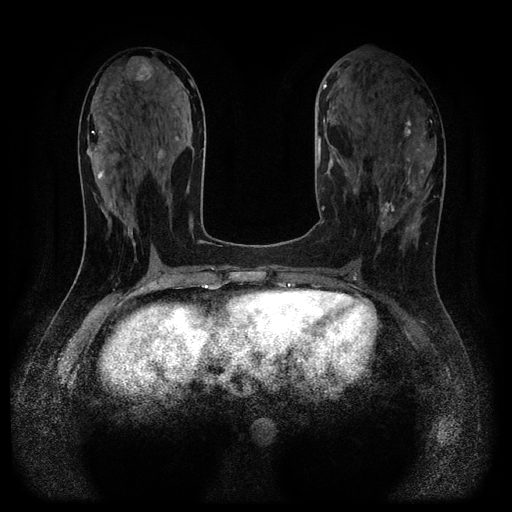
Breast MRI (dynamic contrast-enhanced, multi-phase), one axial slice. Slice 48 of 116 in the series (ordered by position). Dynamic contrast-enhanced series, time point 2 of 5 at this slice position (early post-contrast). 1.5 T. TE 2.7 ms, TR 5.4 ms. 2.2 mm slice thickness. 512 × 512 image matrix. Patient: female, 43 years.
Outlined on this slice (semi-automatic segmentation, software-assisted and operator-edited):
- breast lesion (labelled 'tumour' in the annotation; benign lesions carry a separate 'benign' label): bounding box (x1, y1, x2, y2) in pixels: (377, 201, 396, 234)
- breast lesion (labelled benign in the annotation): (157, 149, 165, 161)
- breast lesion (labelled benign in the annotation): (120, 56, 158, 82)